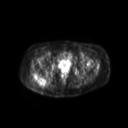
FDG PET of an extremity soft-tissue mass (from a PET/CT study), one axial slice; slice 47 of 267 in the series (ordered by position); 3.27 mm slice thickness; 128 × 128 image matrix, field of view 600 × 600 mm. Female patient, age 60 years. From the clinical record (not read from this slice): histological type: spindle cell suggestive of myxofibrosarcoma; grade: intermediate; site of the primary tumour: right buttock.
Annotated regions visible in this slice (expert contour drawn on MRI and transferred to this co-registered scan by the dataset authors):
- gross tumour volume (mass): box from (x=32, y=72) to (x=48, y=85) px